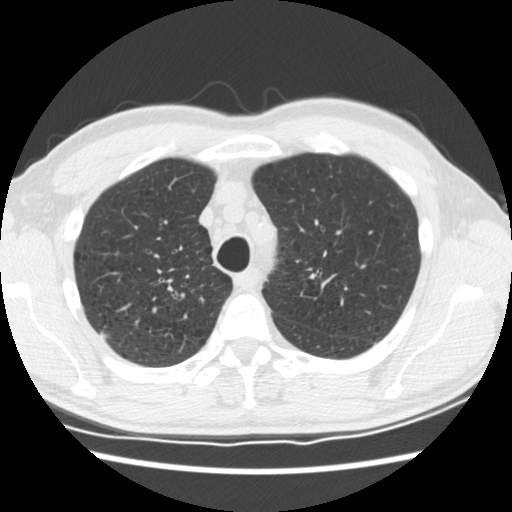
Low-dose screening chest CT, one axial slice. Position 141 of 183 along the scan axis. Reconstruction kernel STANDARD. Lung window (W 1500 / L -600 HU). 2.5 mm slice thickness. 512 × 512 image matrix.
Annotated regions visible in this slice (outlined manually by an expert reader):
- lesion 2 (tumor, upper lobe of right lung): bounding box (x1, y1, x2, y2) in pixels: (100, 331, 109, 340)